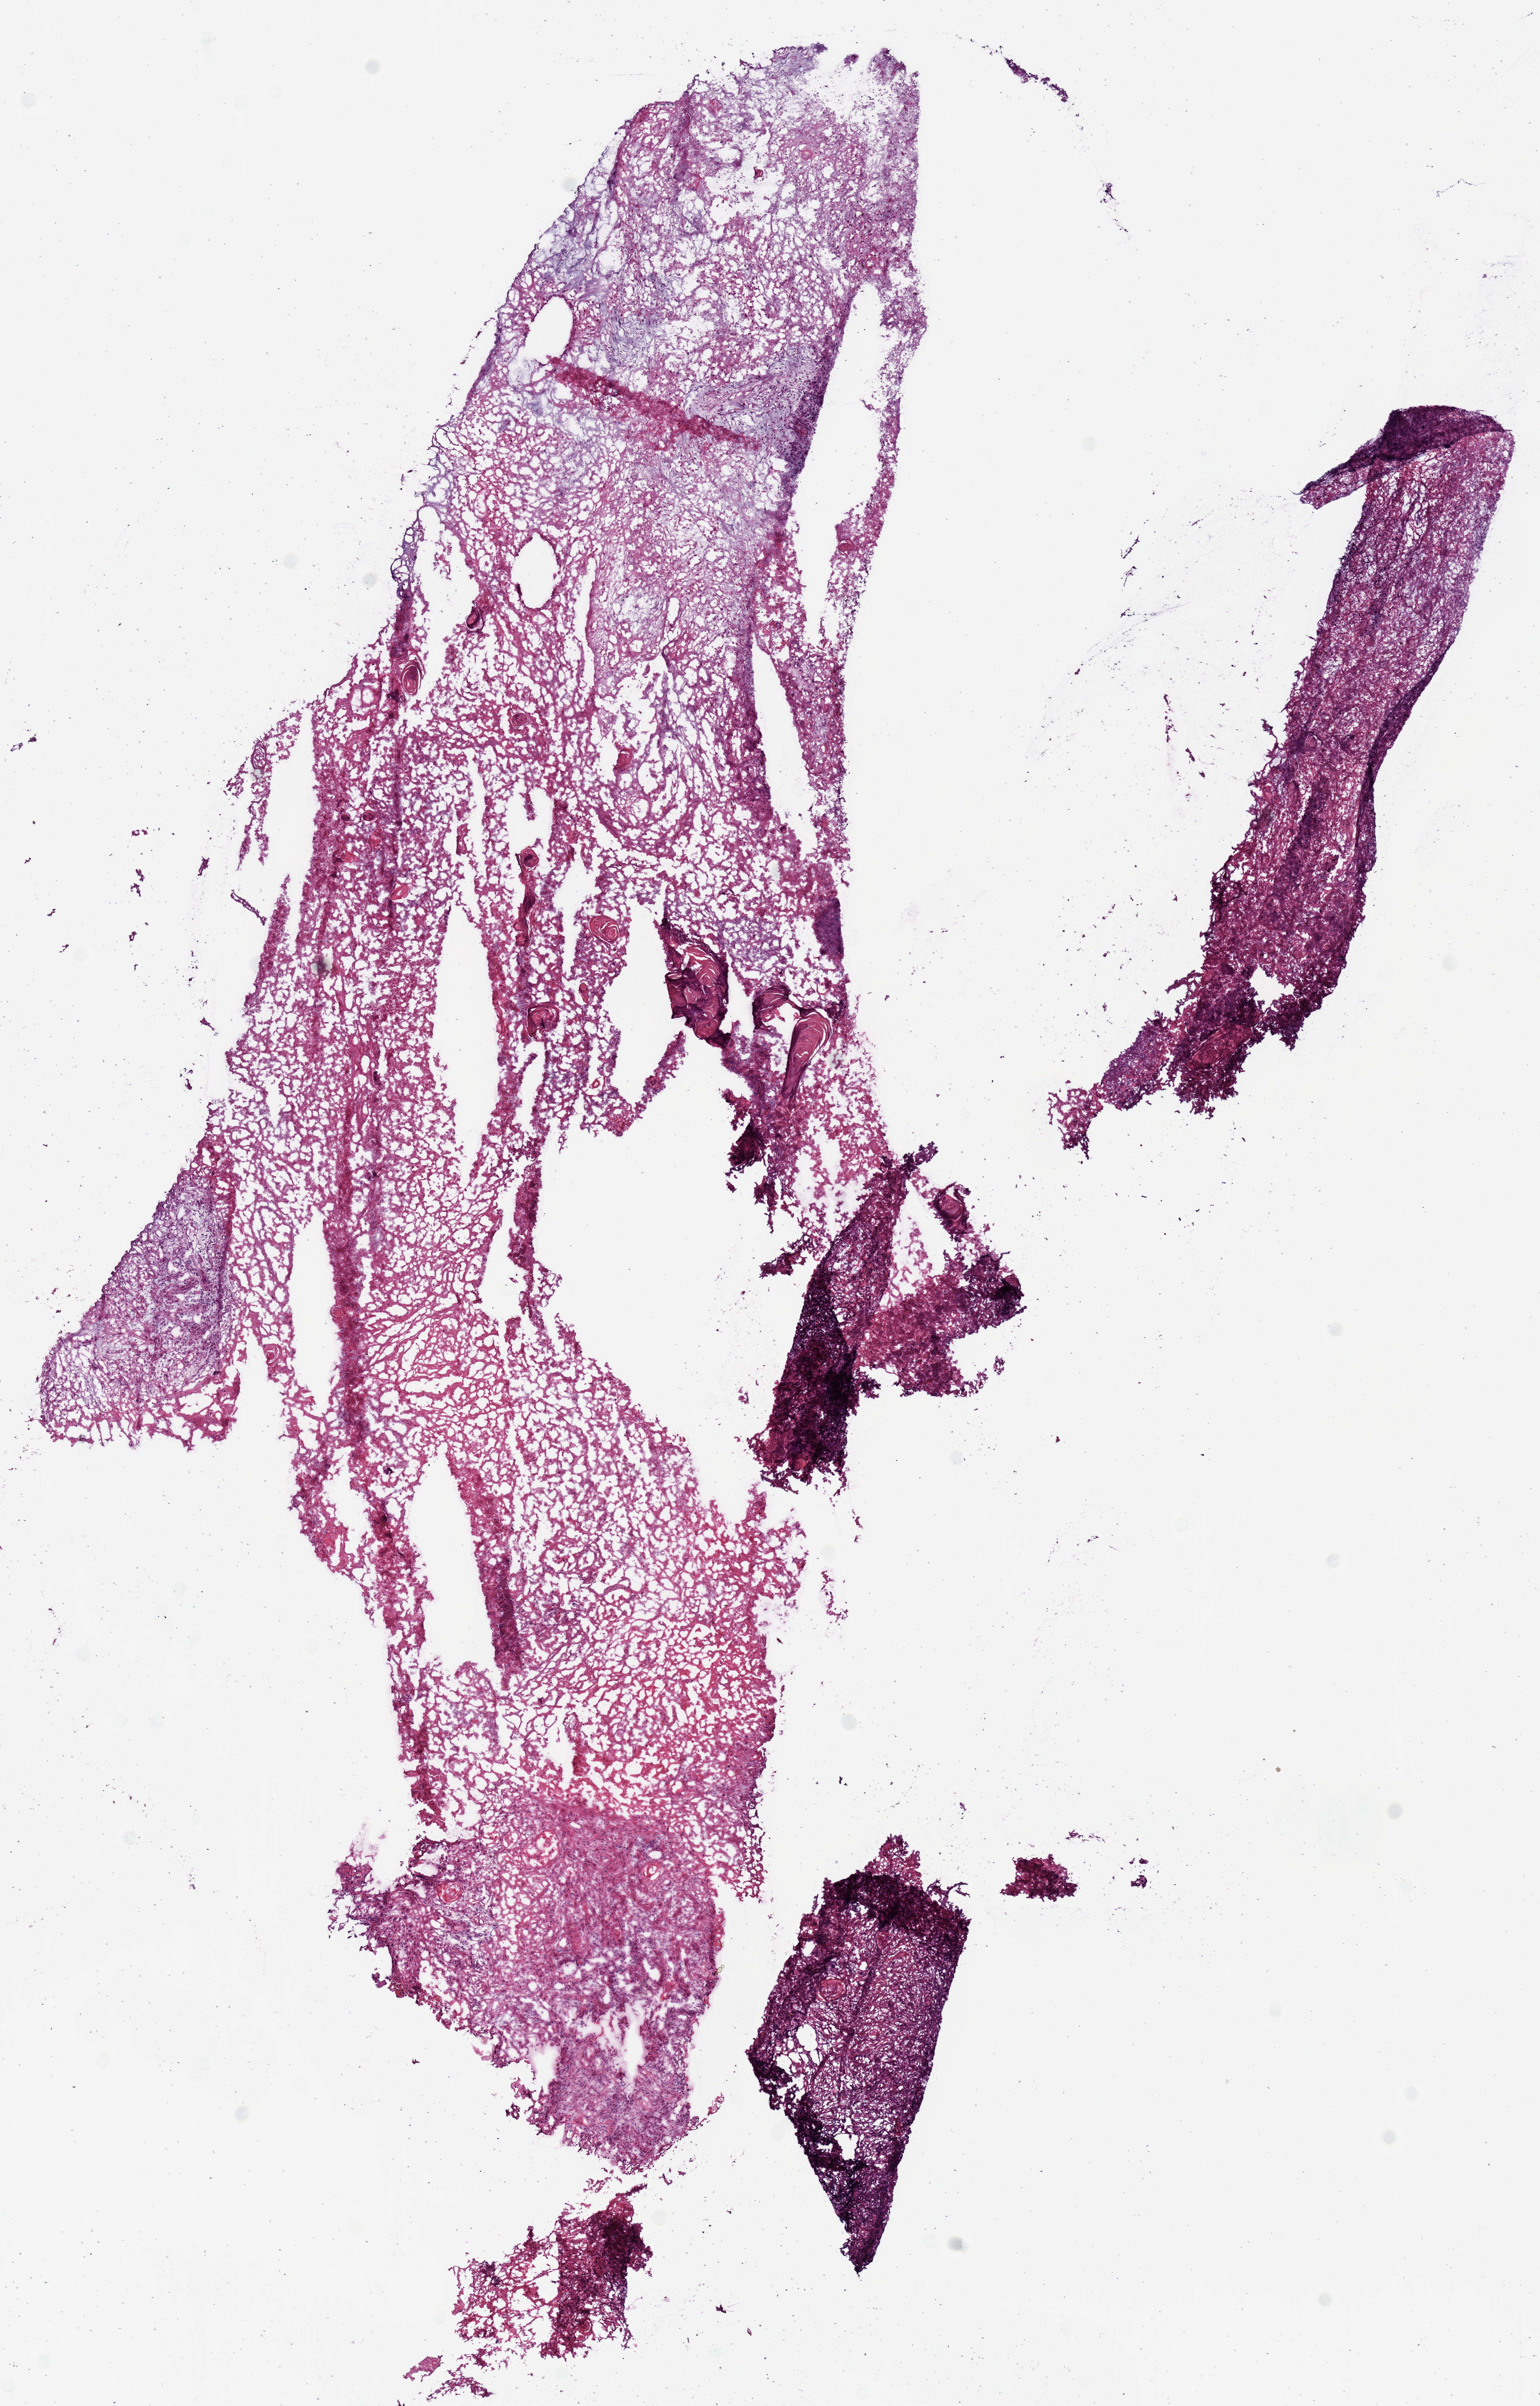
Digitized H&E tissue section (whole slide), whole scanned area (about 7.9 x 12.3 mm) shown as a low-resolution overview, frozen section from the top of the tissue portion, sample: primary tumour, lung. Male patient; age at initial diagnosis 69 years. Pathologist review of this section (percent, as recorded): tumour cells 80%, tumour nuclei 65%.
Diagnosis: Squamous cell carcinoma, NOS (upper lobe, lung).